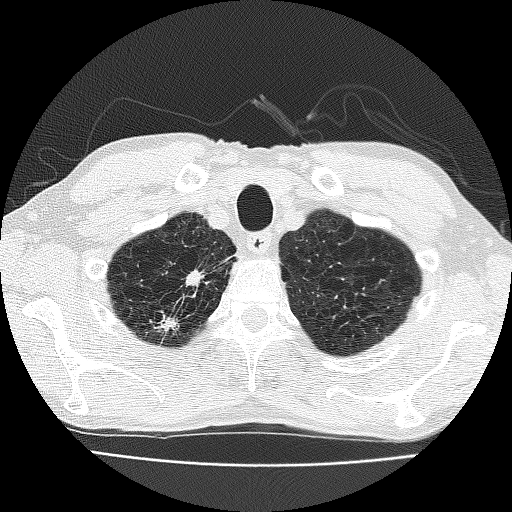
Low-dose screening chest CT, one axial slice; position 156 of 185 along the scan axis; reconstruction kernel FC51; 120 kVp; lung window (W 1500 / L -600 HU); 2 mm slice thickness; 512 × 512 image matrix, field of view 322 × 322 mm.
Structures marked on this image (expert manual segmentation):
- lesion 1 (nodule, upper lobe of right lung): bounding box [x1, y1, x2, y2] px = [186, 270, 203, 286]
- lesion 2 (nodule, upper lobe of right lung): [159, 318, 177, 331]